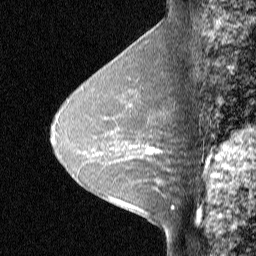
Breast MRI (dynamic contrast-enhanced), one sagittal slice. Position 31 of 48 along the scan axis. Dynamic contrast-enhanced study with each time point stored as its own series, time point 2 of 3 at this slice position (early post-contrast, ordered by acquisition time). 1.5 T. TE 4 ms, TR 30 ms. 3 mm slice thickness. 256 × 256 image matrix, field of view 180 × 180 mm. Patient: female, 31 years. From the clinical record (not read from this slice): setting: breast cancer imaged before/during neoadjuvant chemotherapy; receptor status: HER2-positive.
Outlined on this slice (semi-automatic segmentation, software-assisted and operator-edited):
- analysis volume of interest (the breast-tissue region the enhancement analysis was run in; not a lesion): bounding box [x1, y1, x2, y2] px = [129, 130, 175, 167]
- tumour enhancement mask (voxels above the 90 % enhancement threshold inside the analysis volume of interest): [145, 147, 160, 154]